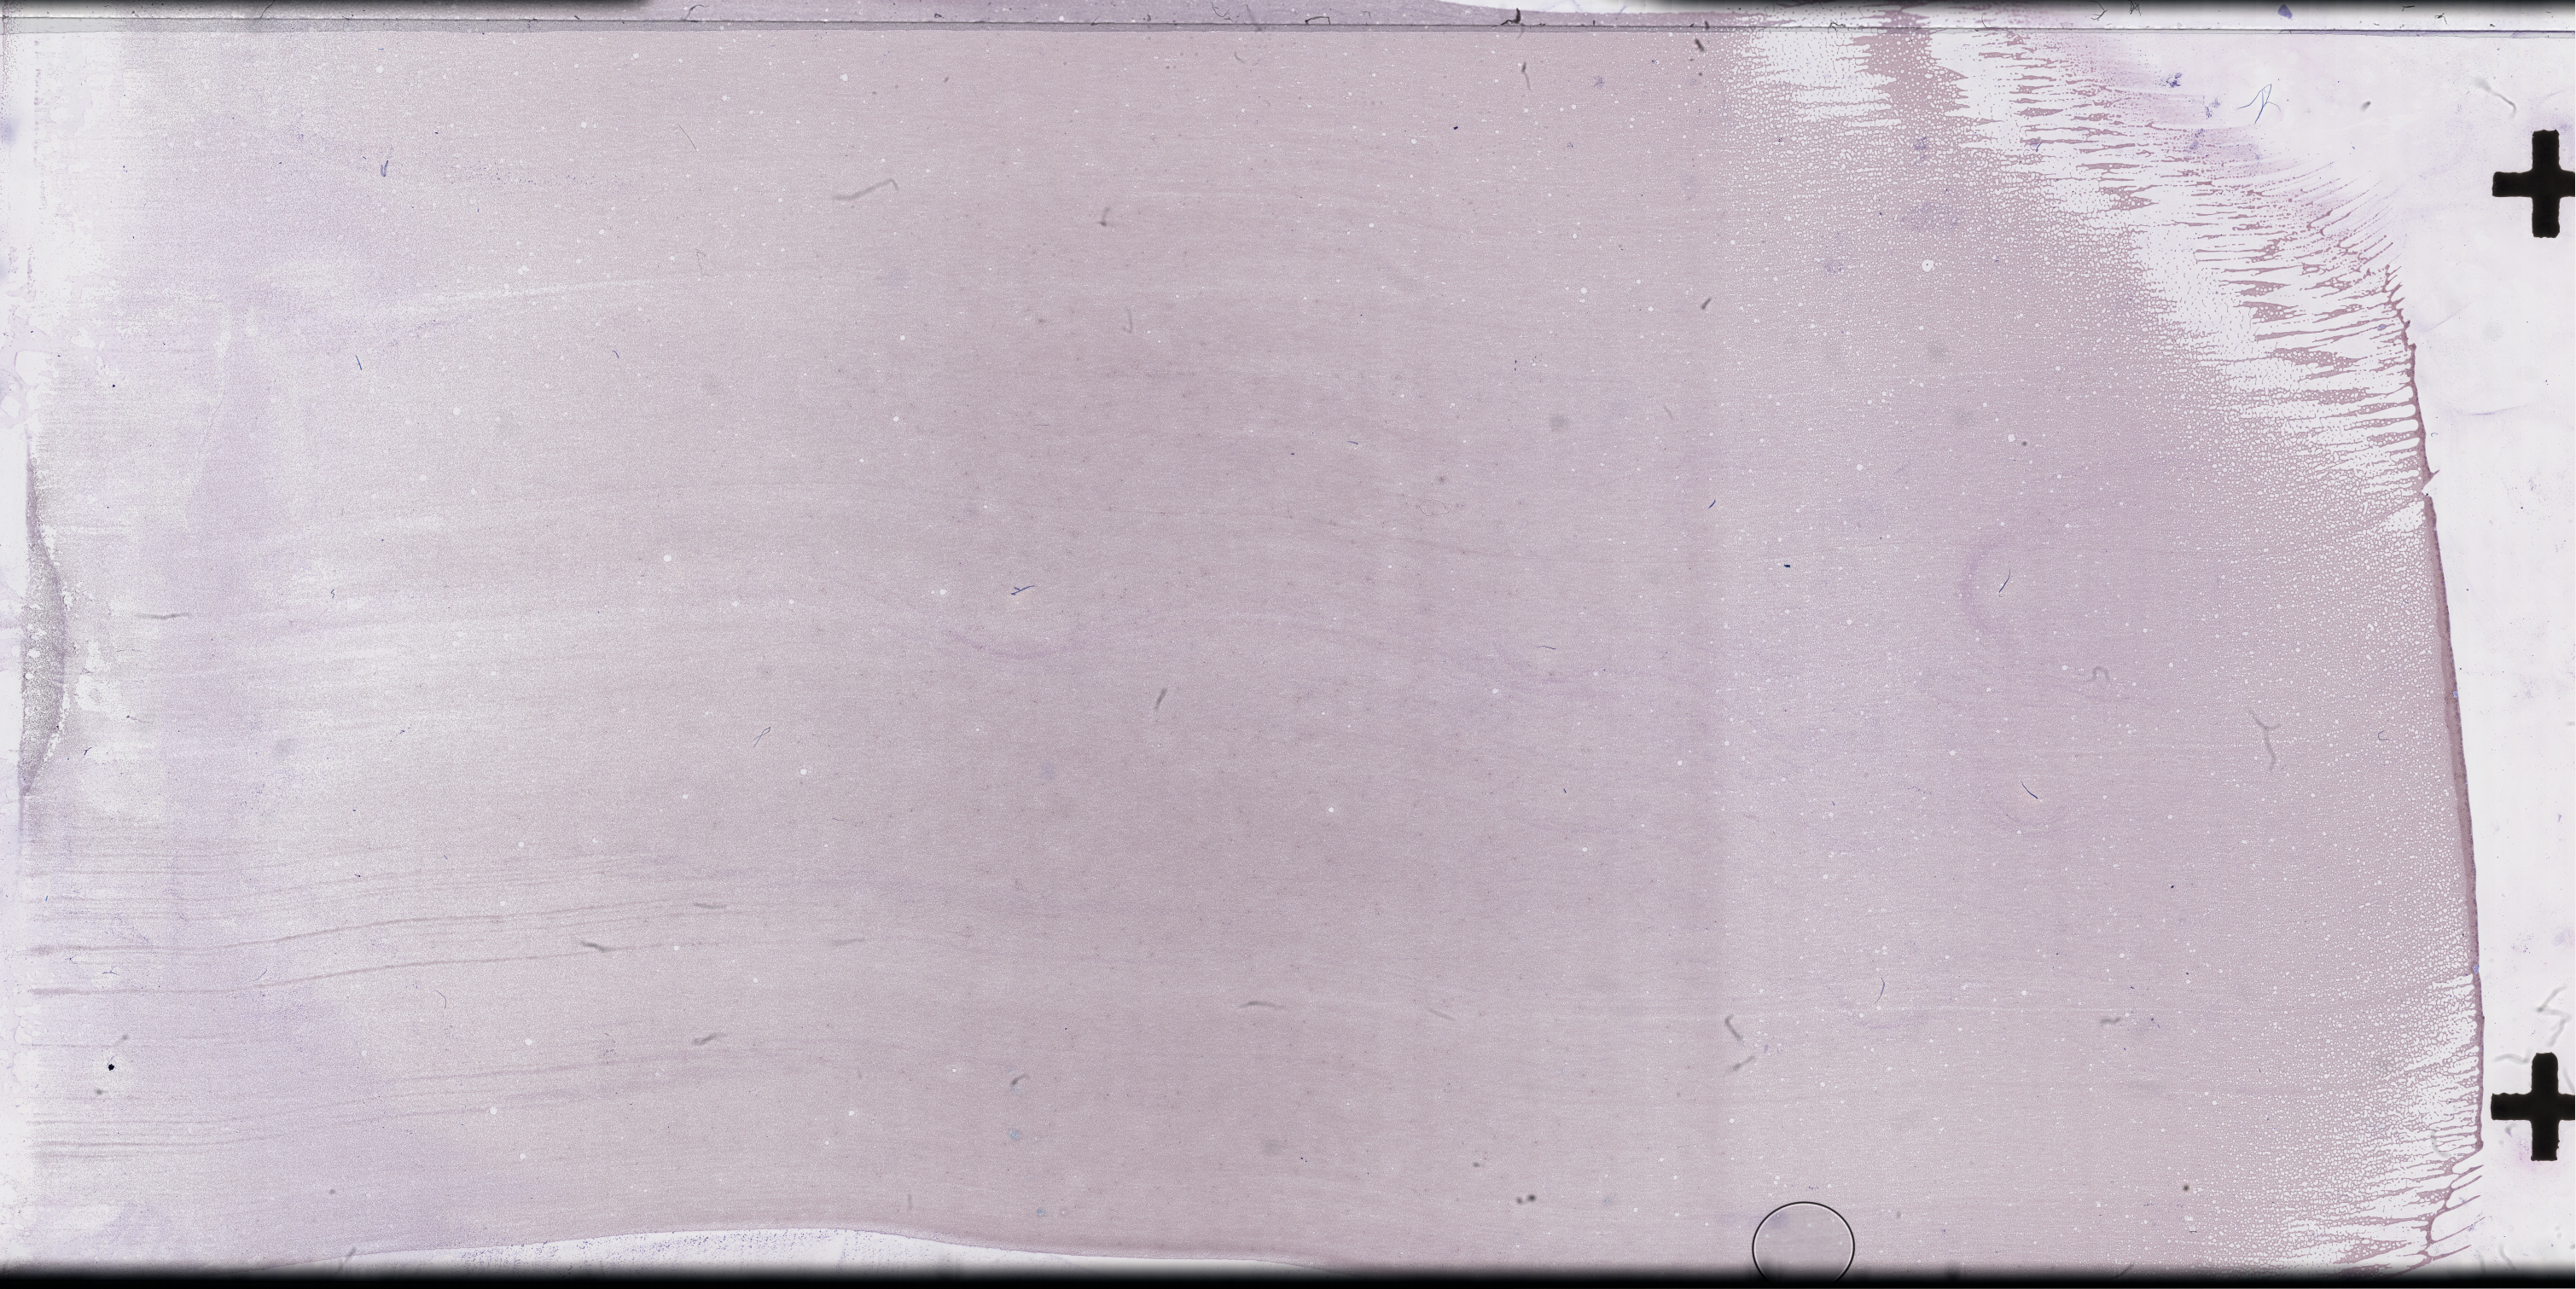
Whole-slide image of a whole blood smear, Wright–Giemsa stain, a low-resolution overview of the entire scanned area, about 48.8 x 24.4 mm, specimen time point: collected on treatment. Patient sex: female.
From a patient with: Plasma Cell Myeloma.